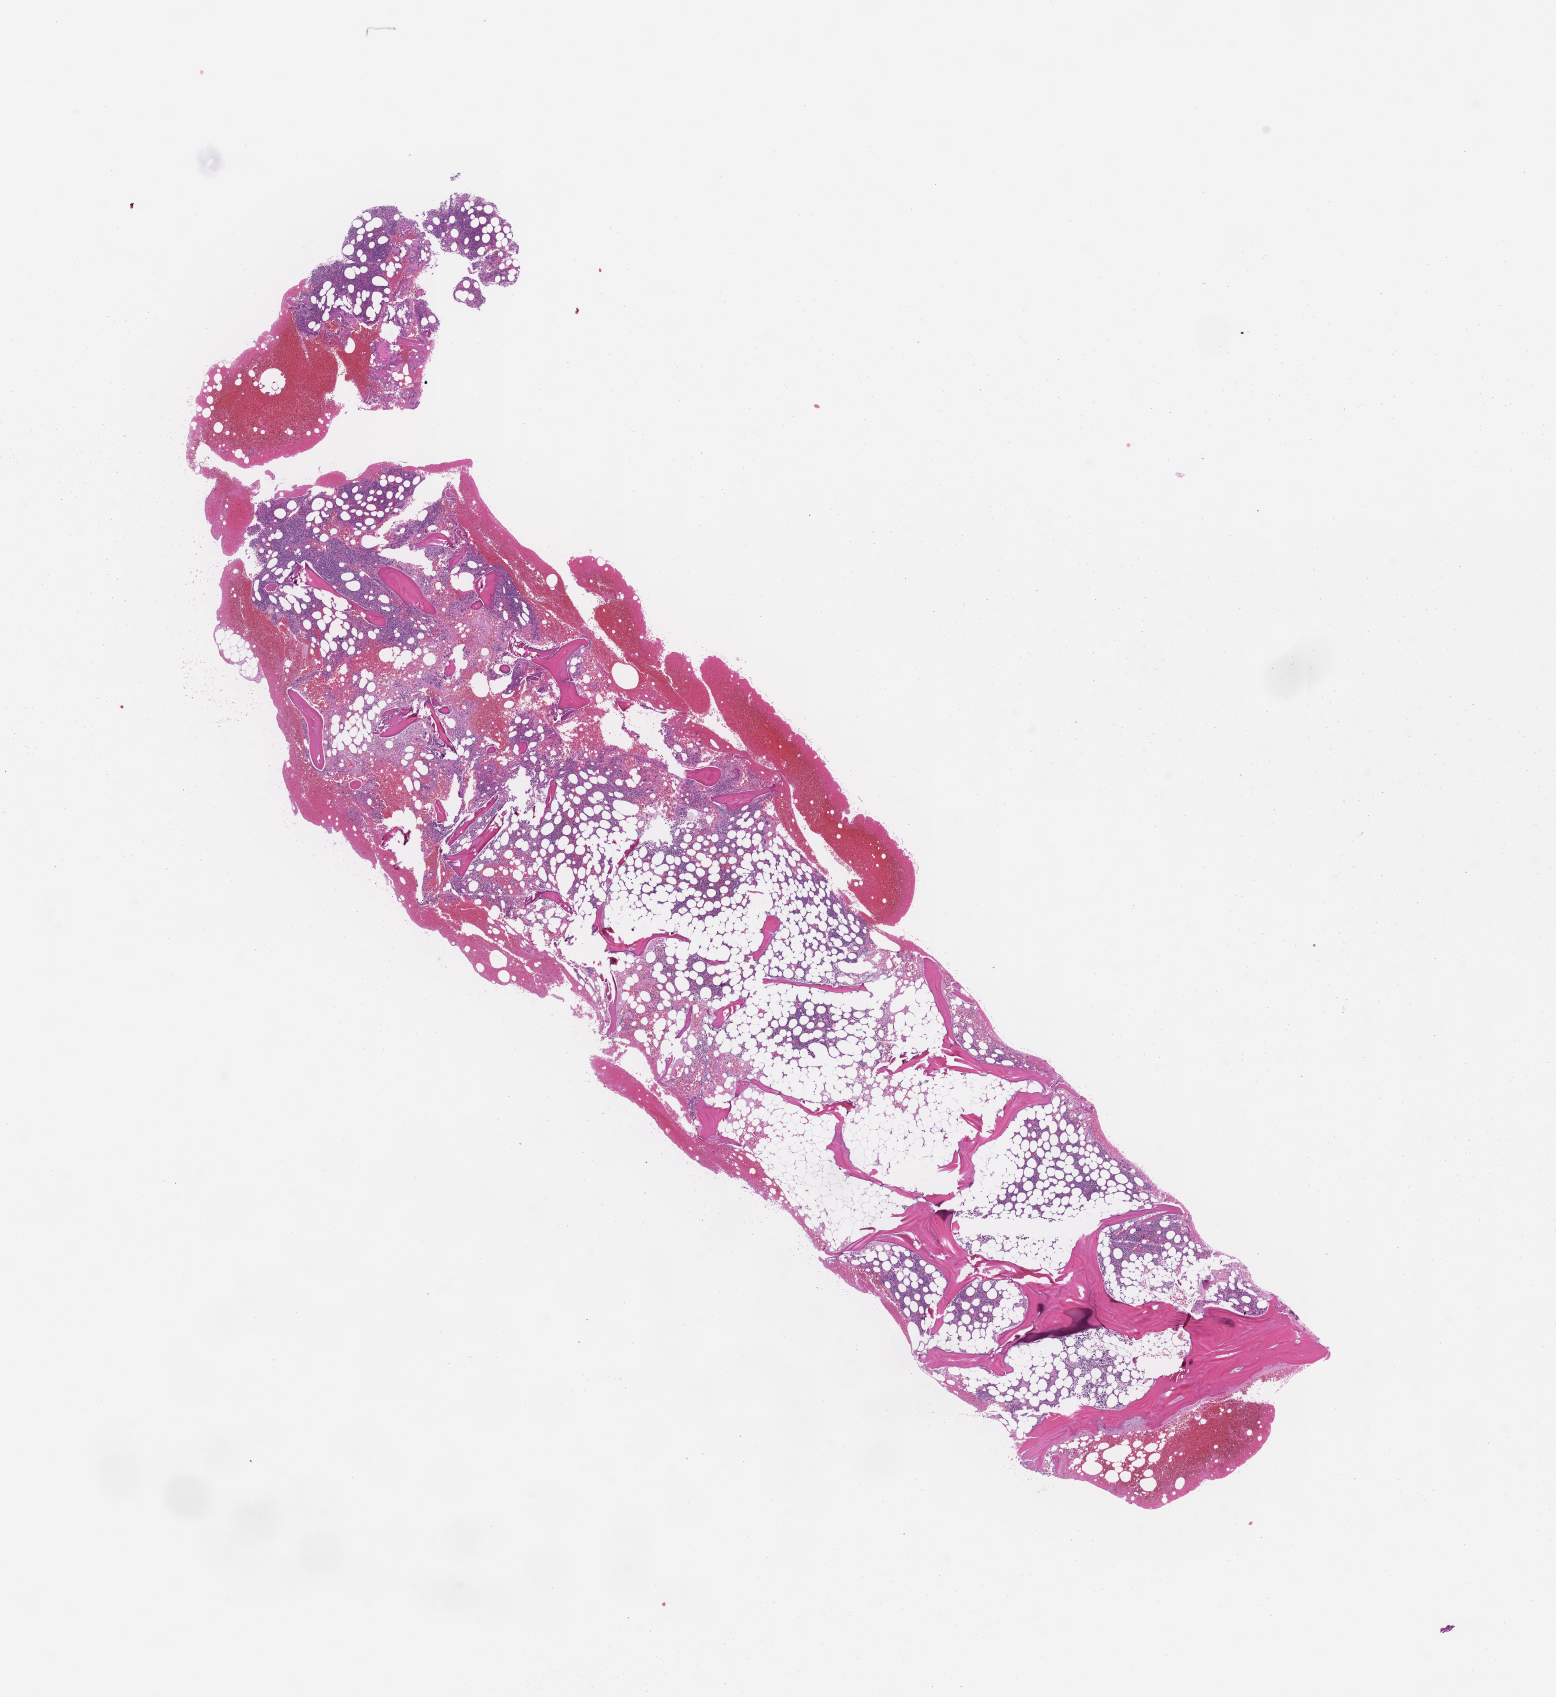
Digitized haematoxylin and eosin-stained section — low-resolution overview of the scanned area, about 12.6 x 13.7 mm; formalin-fixed paraffin-embedded section; site: bone marrow; specimen time point: archival tissue. Patient sex: male.
This section: primary tumour tissue. Diagnosis: Plasma Cell Myeloma.